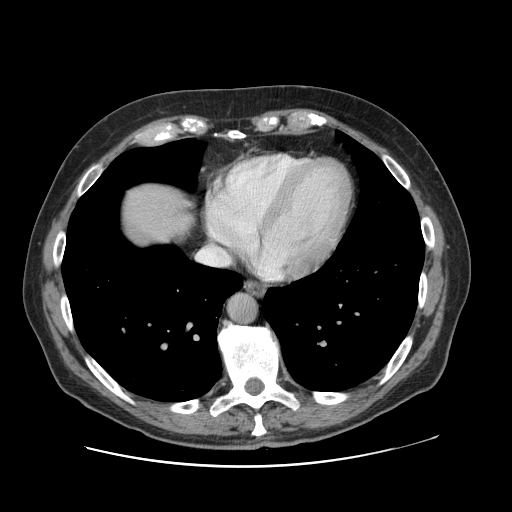
Contrast-enhanced abdominal CT, one axial slice; position 117 of 138 along the scan axis; 120 kVp; intravenous contrast given; soft-tissue window (W 400 / L 40 HU); 2.5 mm slice thickness; 512 × 512 image matrix, field of view 402 × 402 mm. Male patient, age 71 years. Case-level facts recorded for this patient, not image findings: diagnosis: colorectal cancer liver metastases, imaged before liver resection; multiple liver metastases: no; largest metastasis: 3.3 cm; chemotherapy before resection: no.
Structures marked on this image (manually delineated by an expert):
- liver: bounding box (x1, y1, x2, y2) in pixels: (120, 181, 194, 246)
- planned liver remnant (the part of the liver to remain after resection): (119, 181, 192, 246)